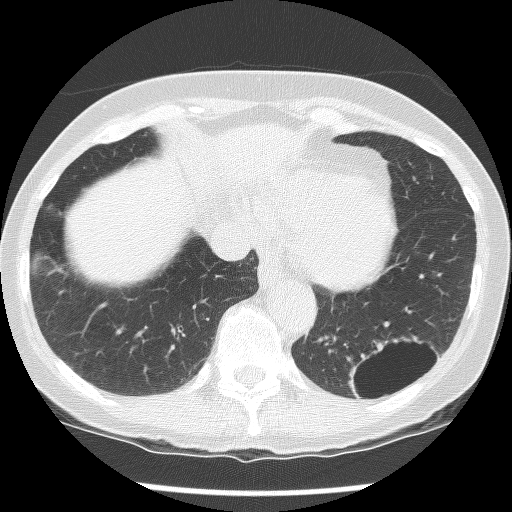
Low-dose screening chest CT, axial slice, second annual screen, lung window (W 1500 / L -600 HU), 120 kVp, slice 98 of 136 in the series, 512 × 512 image matrix. Female, age 61 years at enrolment. Current smoker at enrolment.
Lesion marked by an expert reader, box from (x=329, y=317) to (x=438, y=414) px. The screening reader recorded 2 non-calcified nodules or masses ≥4 mm on this exam (left lower lobe, left lower lobe); which of them this box marks is not recorded. Lung cancer was diagnosed 585 days after this screen: non-small cell carcinoma, left lower lobe, poorly differentiated (G3), stage IB (AJCC 6th edition), 100 mm at pathology.